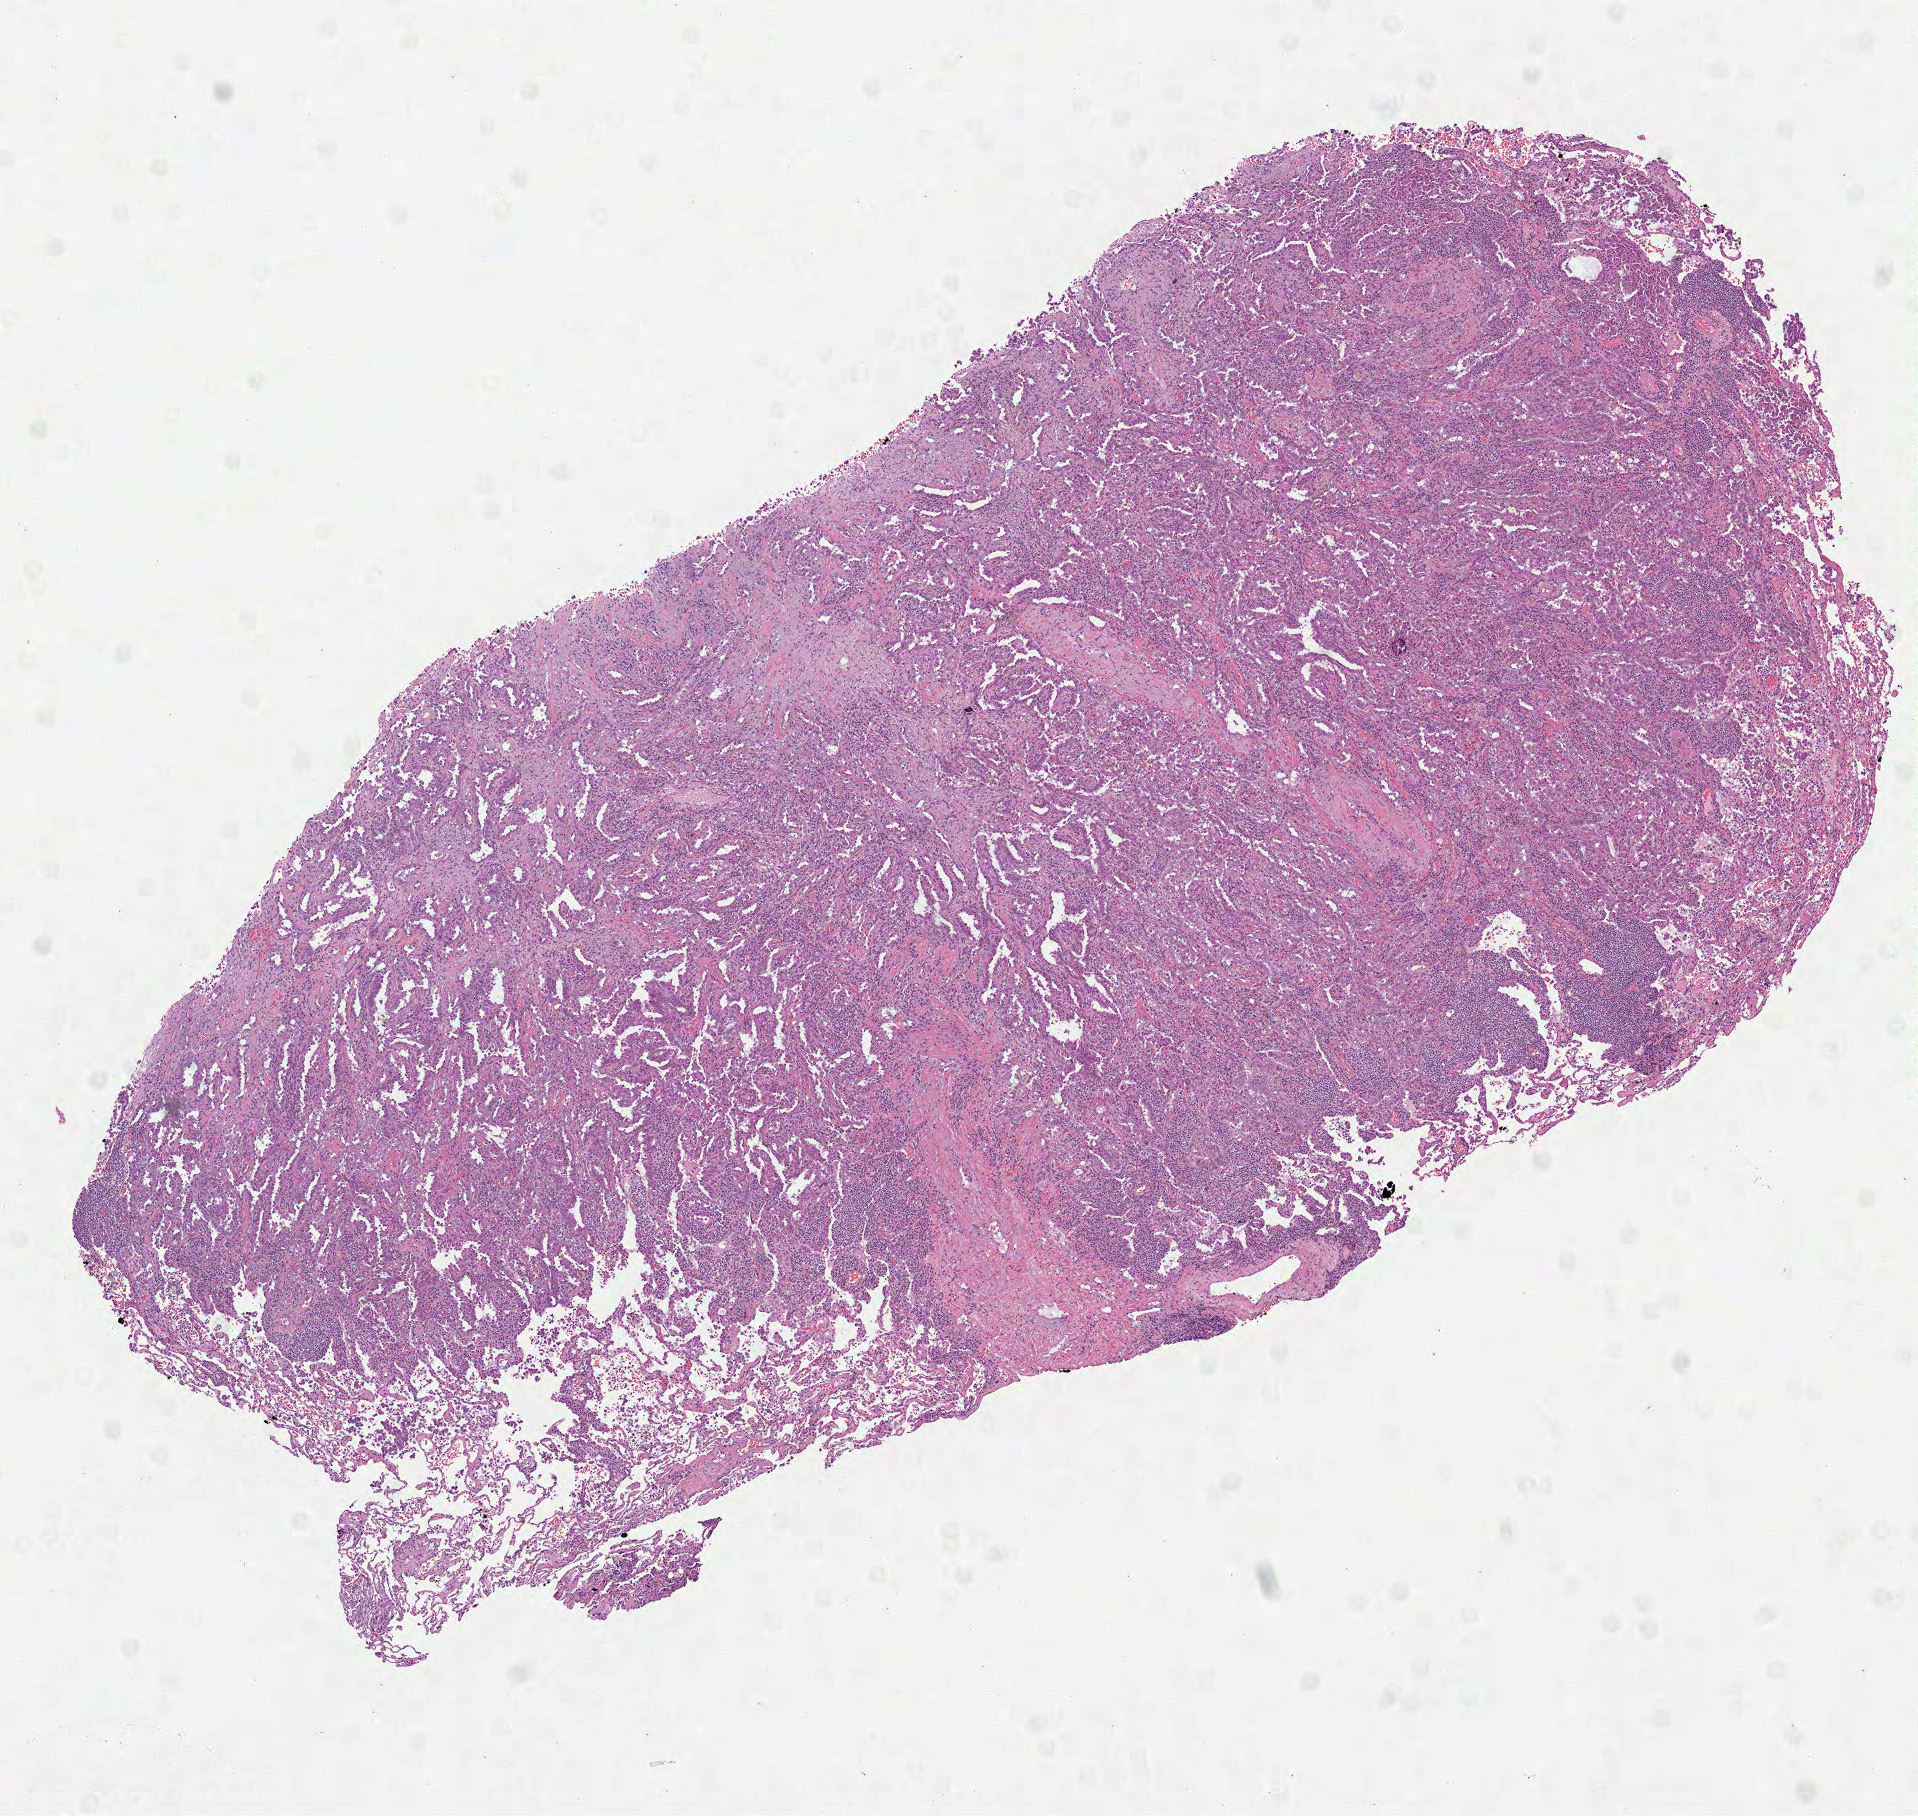
H&E-stained whole-slide image, shown as a low-resolution overview of the whole scanned area (about 7.7 x 7.3 mm, slide scanned at 40x); formalin-fixed paraffin-embedded (FFPE) diagnostic section; primary tumour sample from the lung. Patient: female, age at initial diagnosis 71 years.
• diagnosis: Adenocarcinoma, NOS (upper lobe, lung)
• TNM: T1b N1 MX
• AJCC pathologic stage: IIA (7th edition)